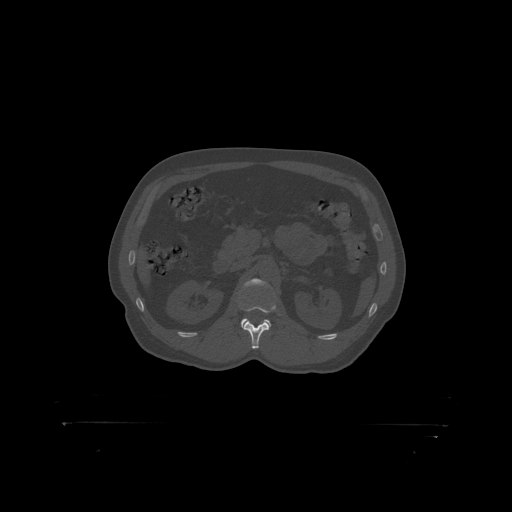
CT including the spine, one axial slice. Position 314 of 399 along the scan axis. Reconstruction kernel STANDARD. Bone window (W 1800 / L 400 HU). 1.25 mm slice thickness. 512 × 512 image matrix, field of view 650 × 650 mm. Male patient, age 46 years. From the clinical record (not read from this slice): primary cancer: skin.
Outlined on this slice (semi-automatic segmentation, software-assisted and operator-edited):
- L1 vertebra: bounding box (x1, y1, x2, y2) in pixels: (239, 305, 276, 313)
- L2 vertebra: (243, 279, 265, 289)